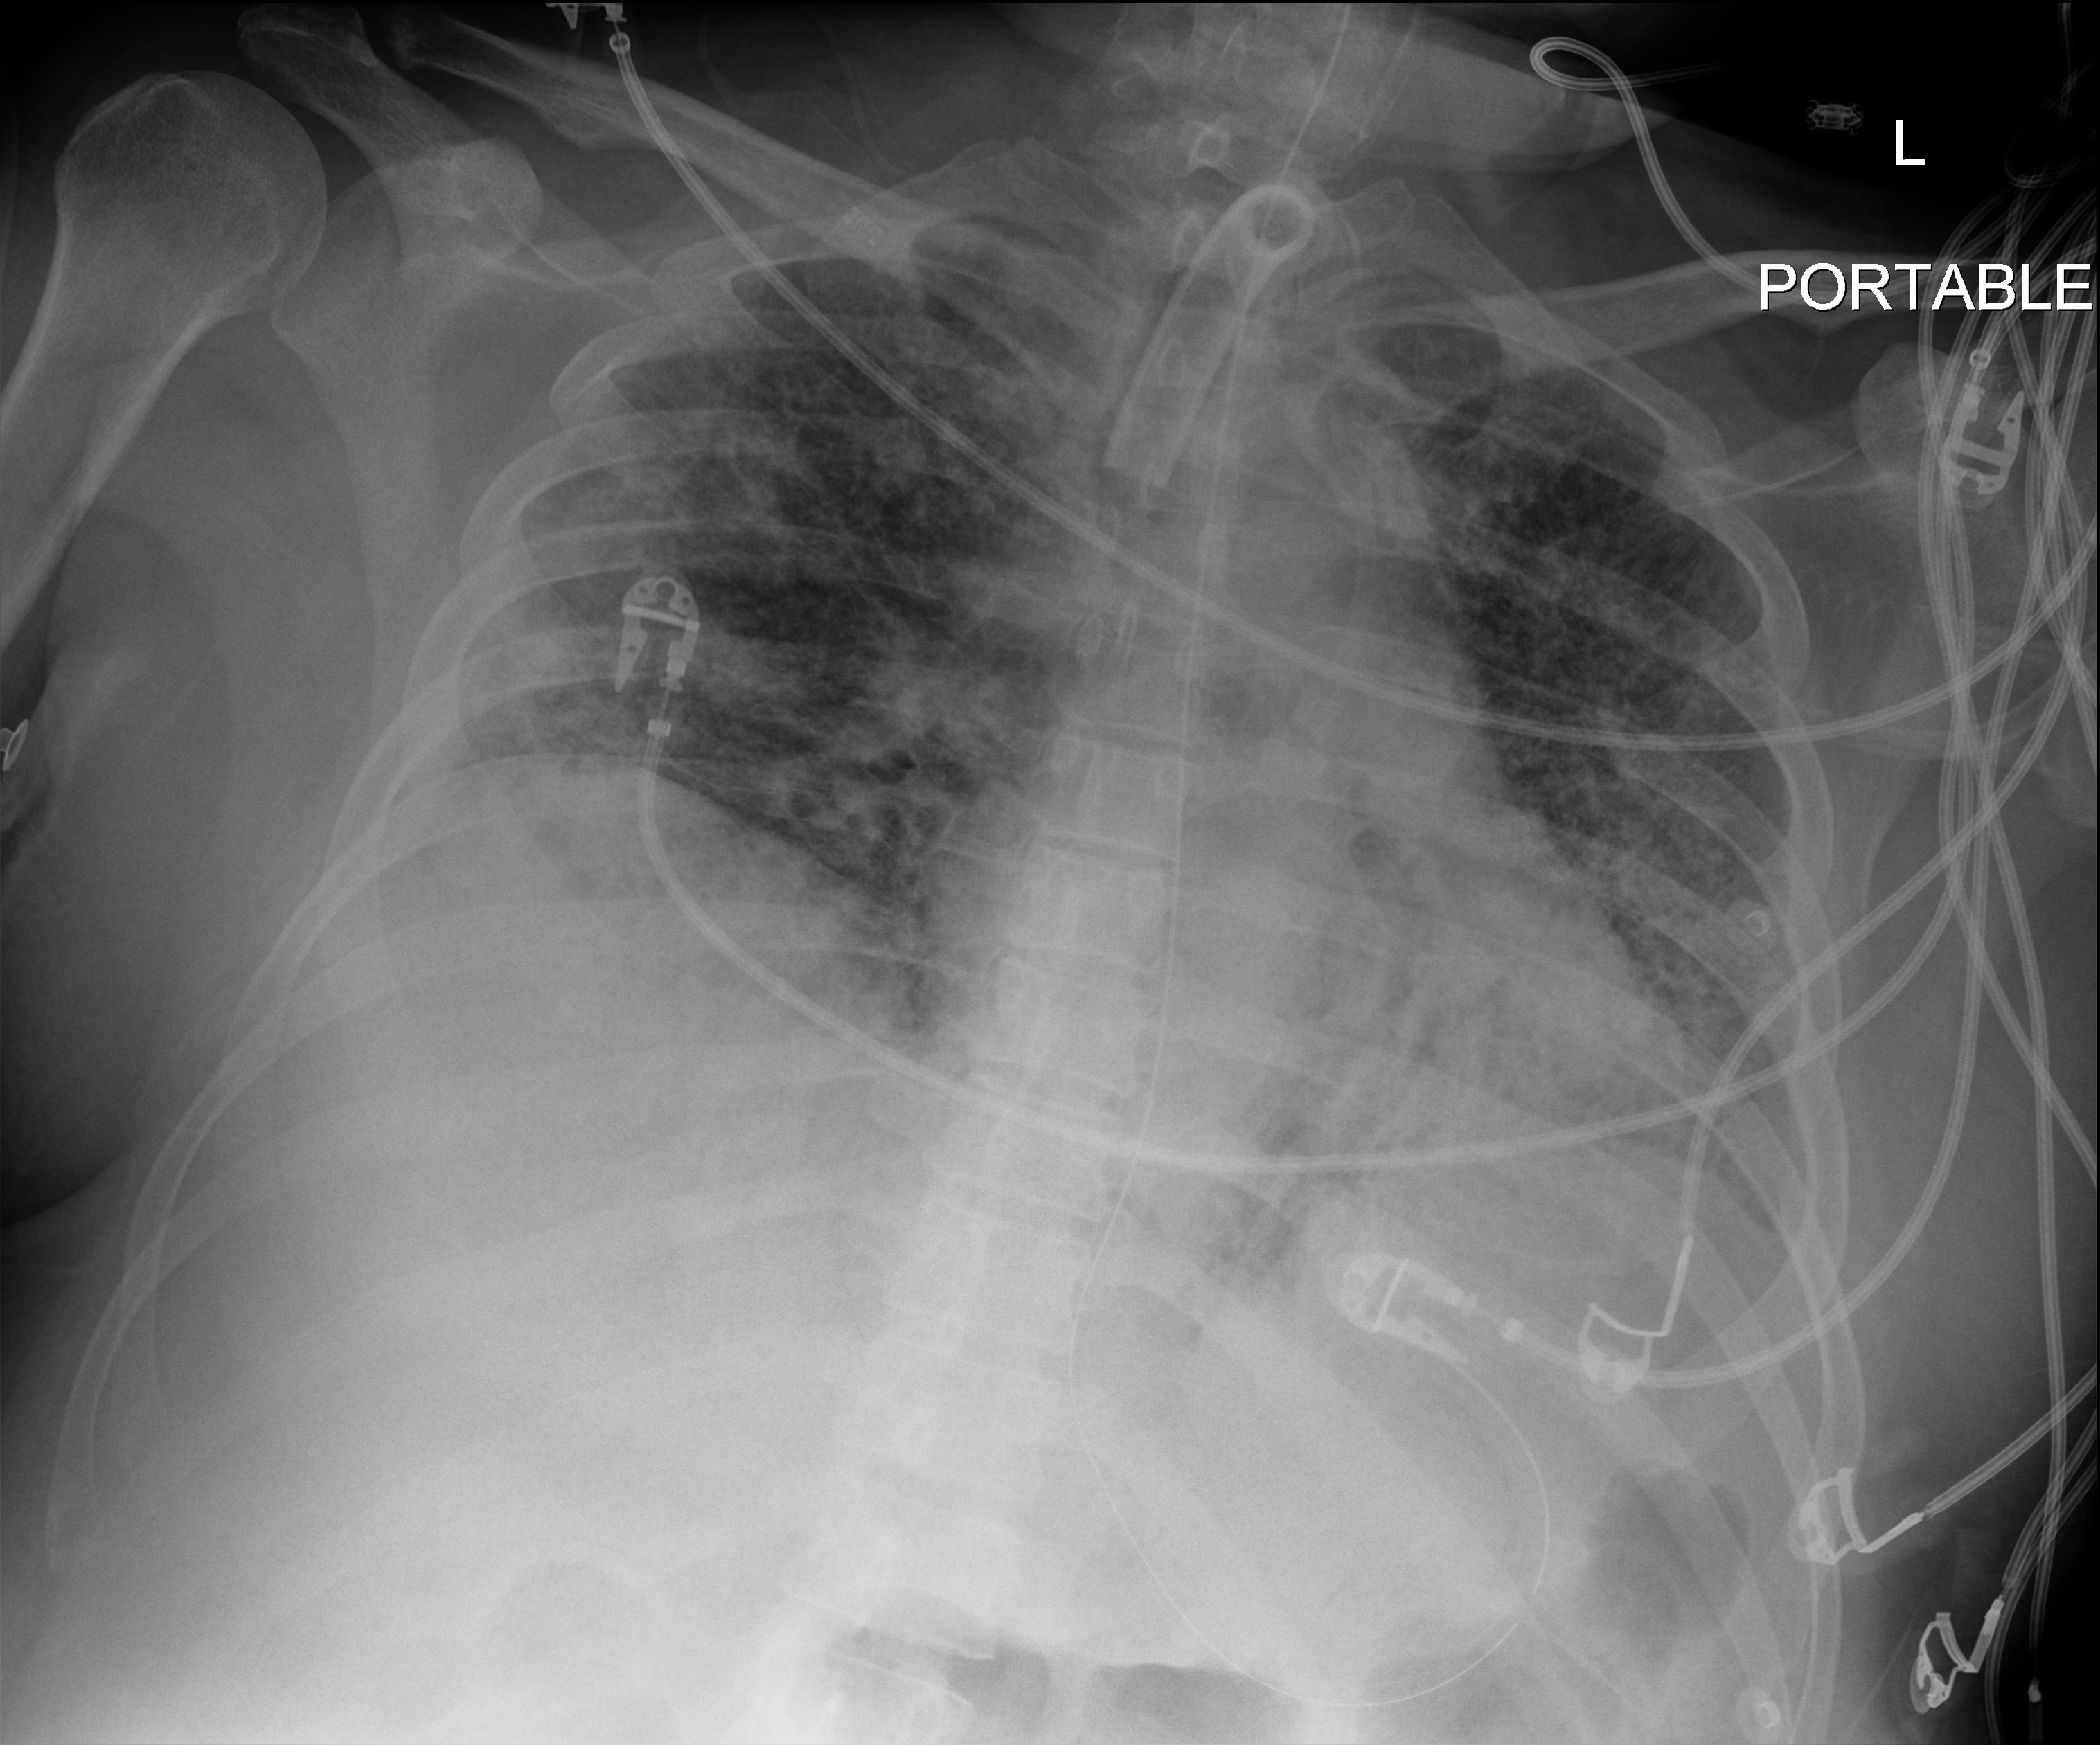
Bedside chest radiograph (digital radiography); anteroposterior (AP) projection. Patient hospitalised with COVID-19; male, aged 18–59 years.
Hospital-stay facts (about this admission, not read from this image; timing relative to this image not recorded):
- chronic kidney disease (admission record): no
- admitted to intensive care during this hospital stay: yes